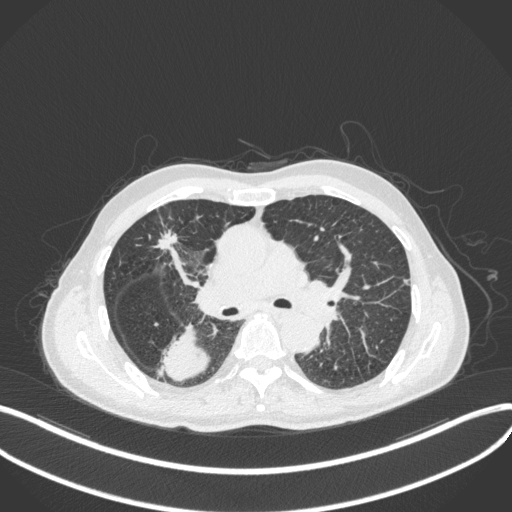
Chest CT, one axial slice. Slice 273 of 423 in the series (ordered by position). Reconstruction kernel B31f. 120 kVp. Lung window (W 1500 / L -600 HU). 1 mm slice thickness. 512 × 512 image matrix, field of view 400 × 400 mm. Patient: male, 79 years. Case-level facts recorded for this patient, not image findings: clinical TNM (as recorded): T3 N0 M0.
Structures marked on this image (bounding box drawn by a radiologist):
- lung tumour (recorded histology: adenocarcinoma): bounding box [x1, y1, x2, y2] px = [155, 323, 214, 383]